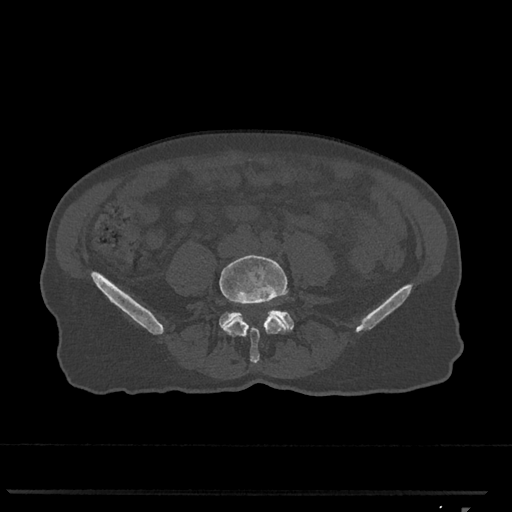
CT including the spine, one axial slice. Position 187 of 793 along the scan axis. 120 kVp. Bone window (W 1800 / L 400 HU). 0.5 mm slice thickness. 512 × 512 image matrix, field of view 380 × 380 mm. Female patient, age 62 years. Case-level facts recorded for this patient, not image findings: primary cancer: renal.
Outlined on this slice (semi-automatically segmented with operator editing):
- L4 vertebra: bounding box (x1, y1, x2, y2) in pixels: (219, 255, 290, 364)
- L5 vertebra: (219, 310, 294, 330)